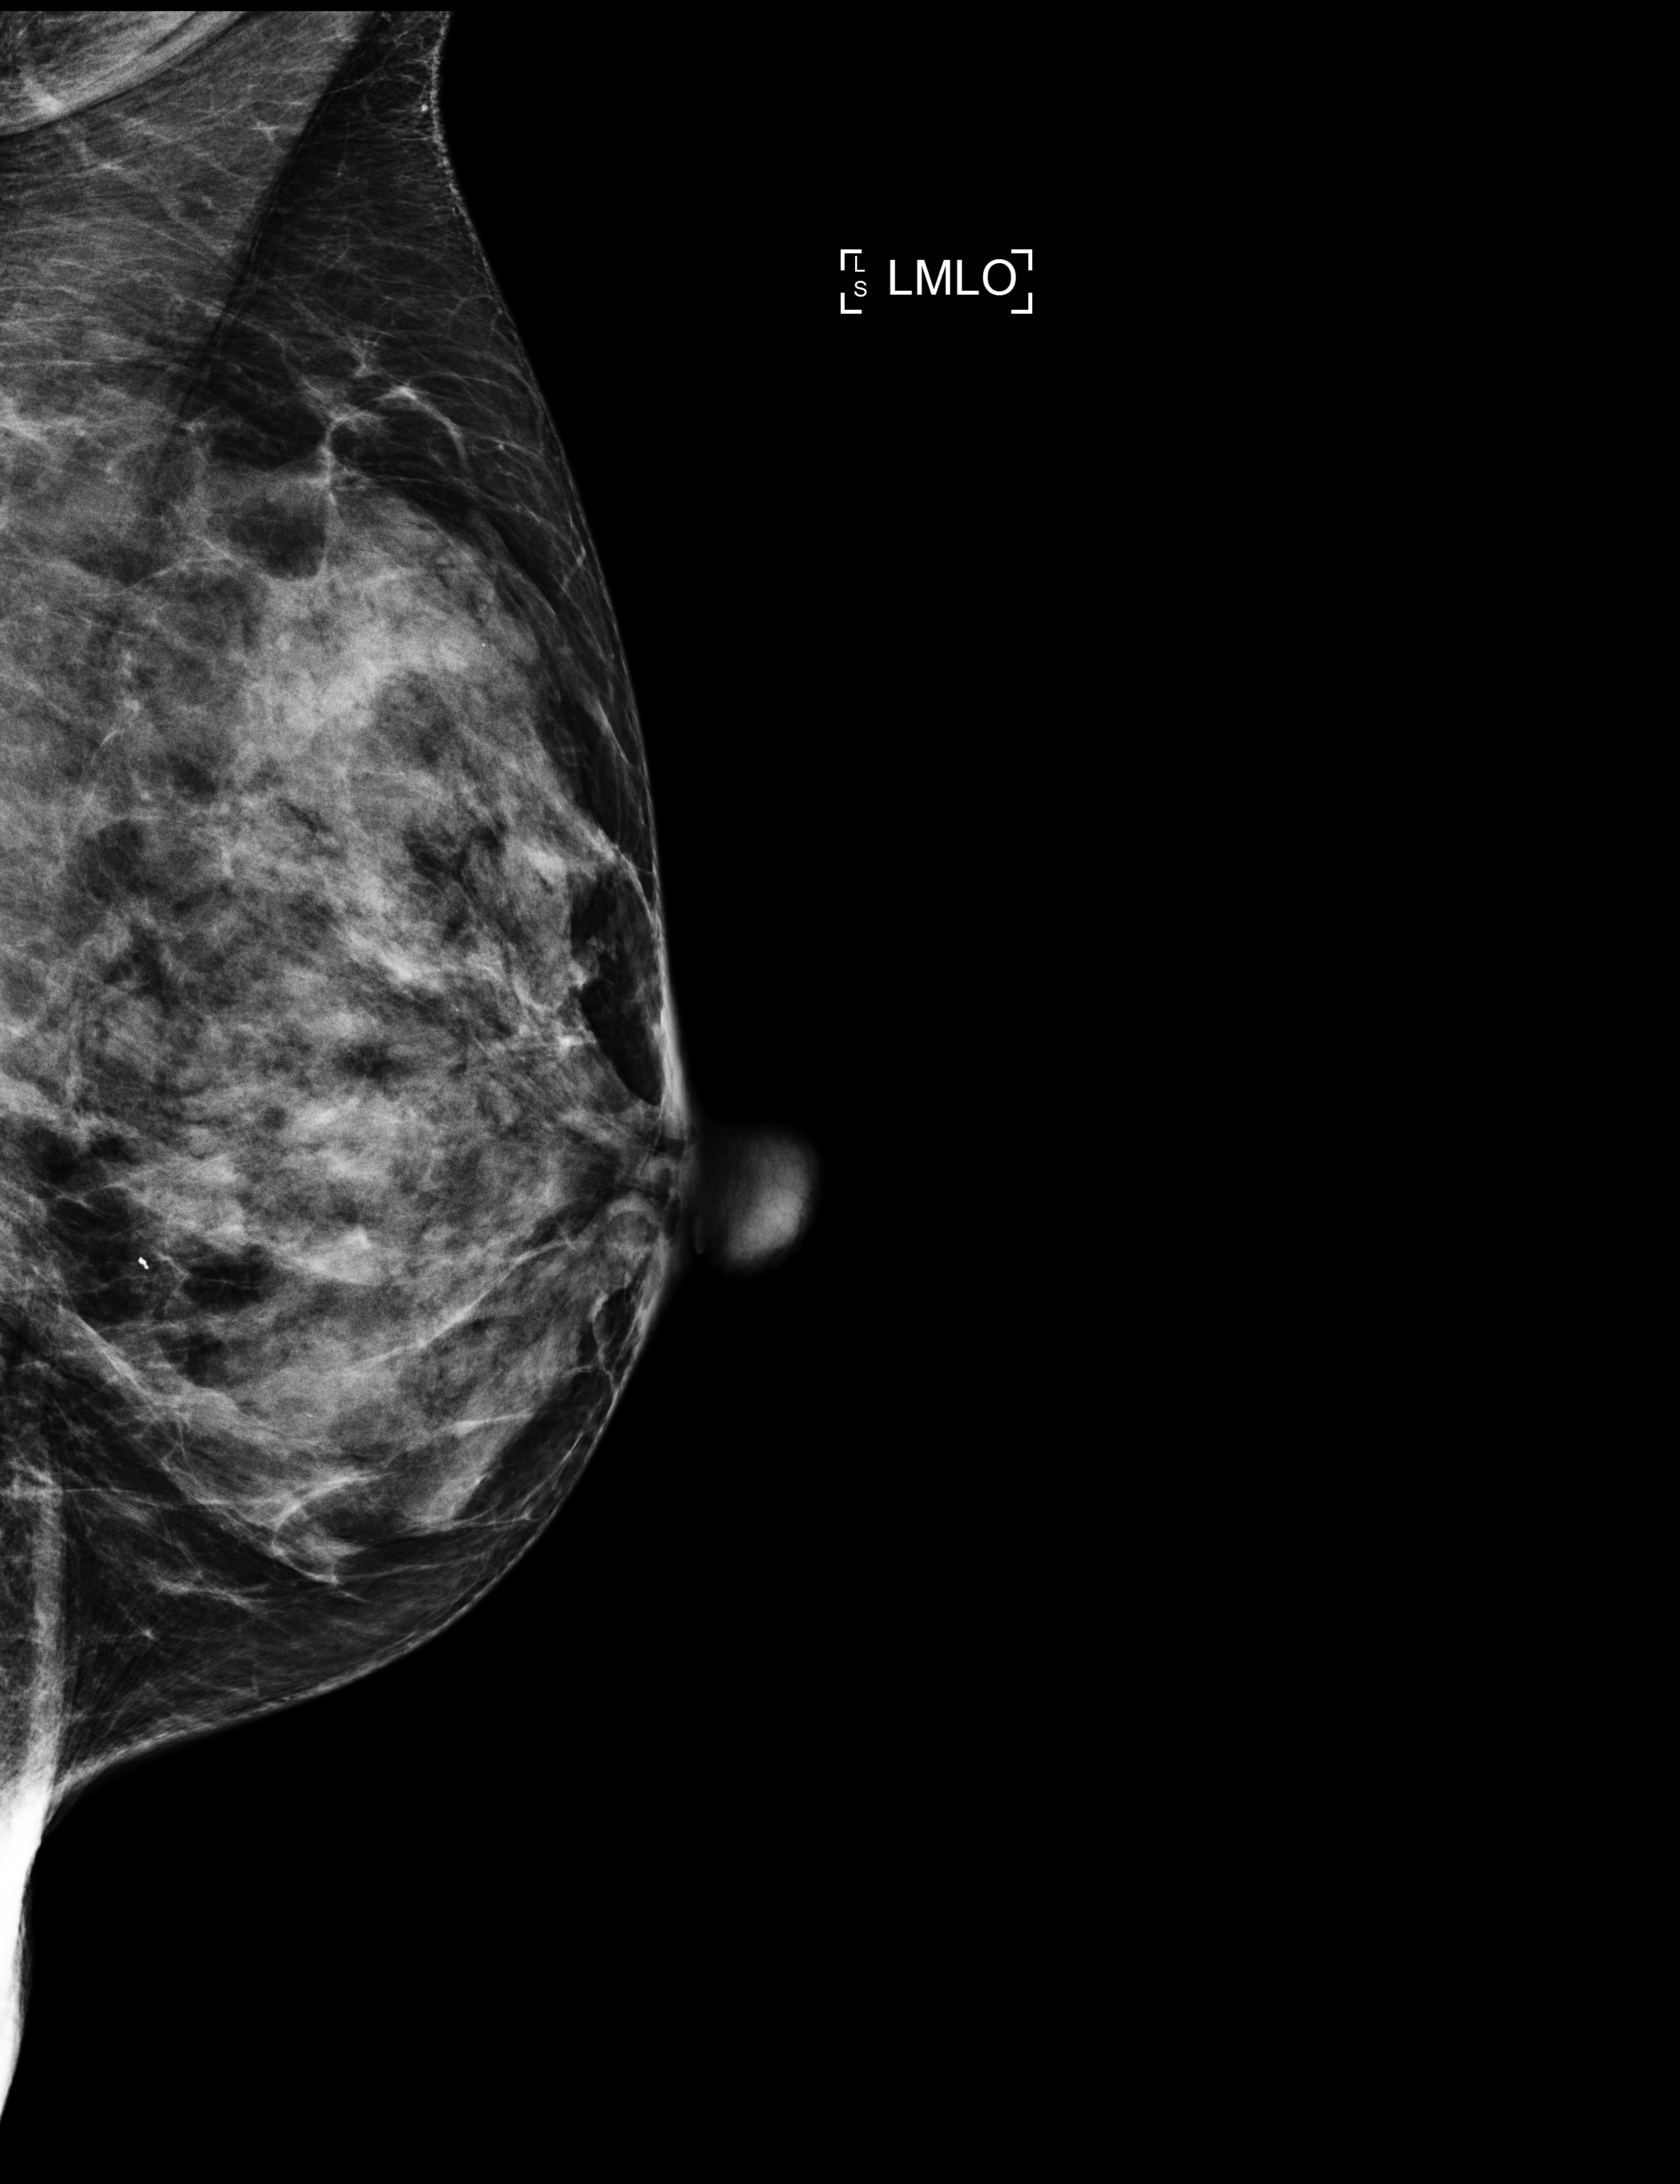
Digital mammogram (FFDM); left breast; mediolateral oblique (MLO) view; annual screening mammography examination; system: Selenia Dimensions. Patient aged 67 years (female).
Breast density at the screening exam (both breasts): extremely dense (BI-RADS density category d). Final BI-RADS category for the screening round (tomosynthesis exam, both breasts): category 2. Recall: no recall after this screen.